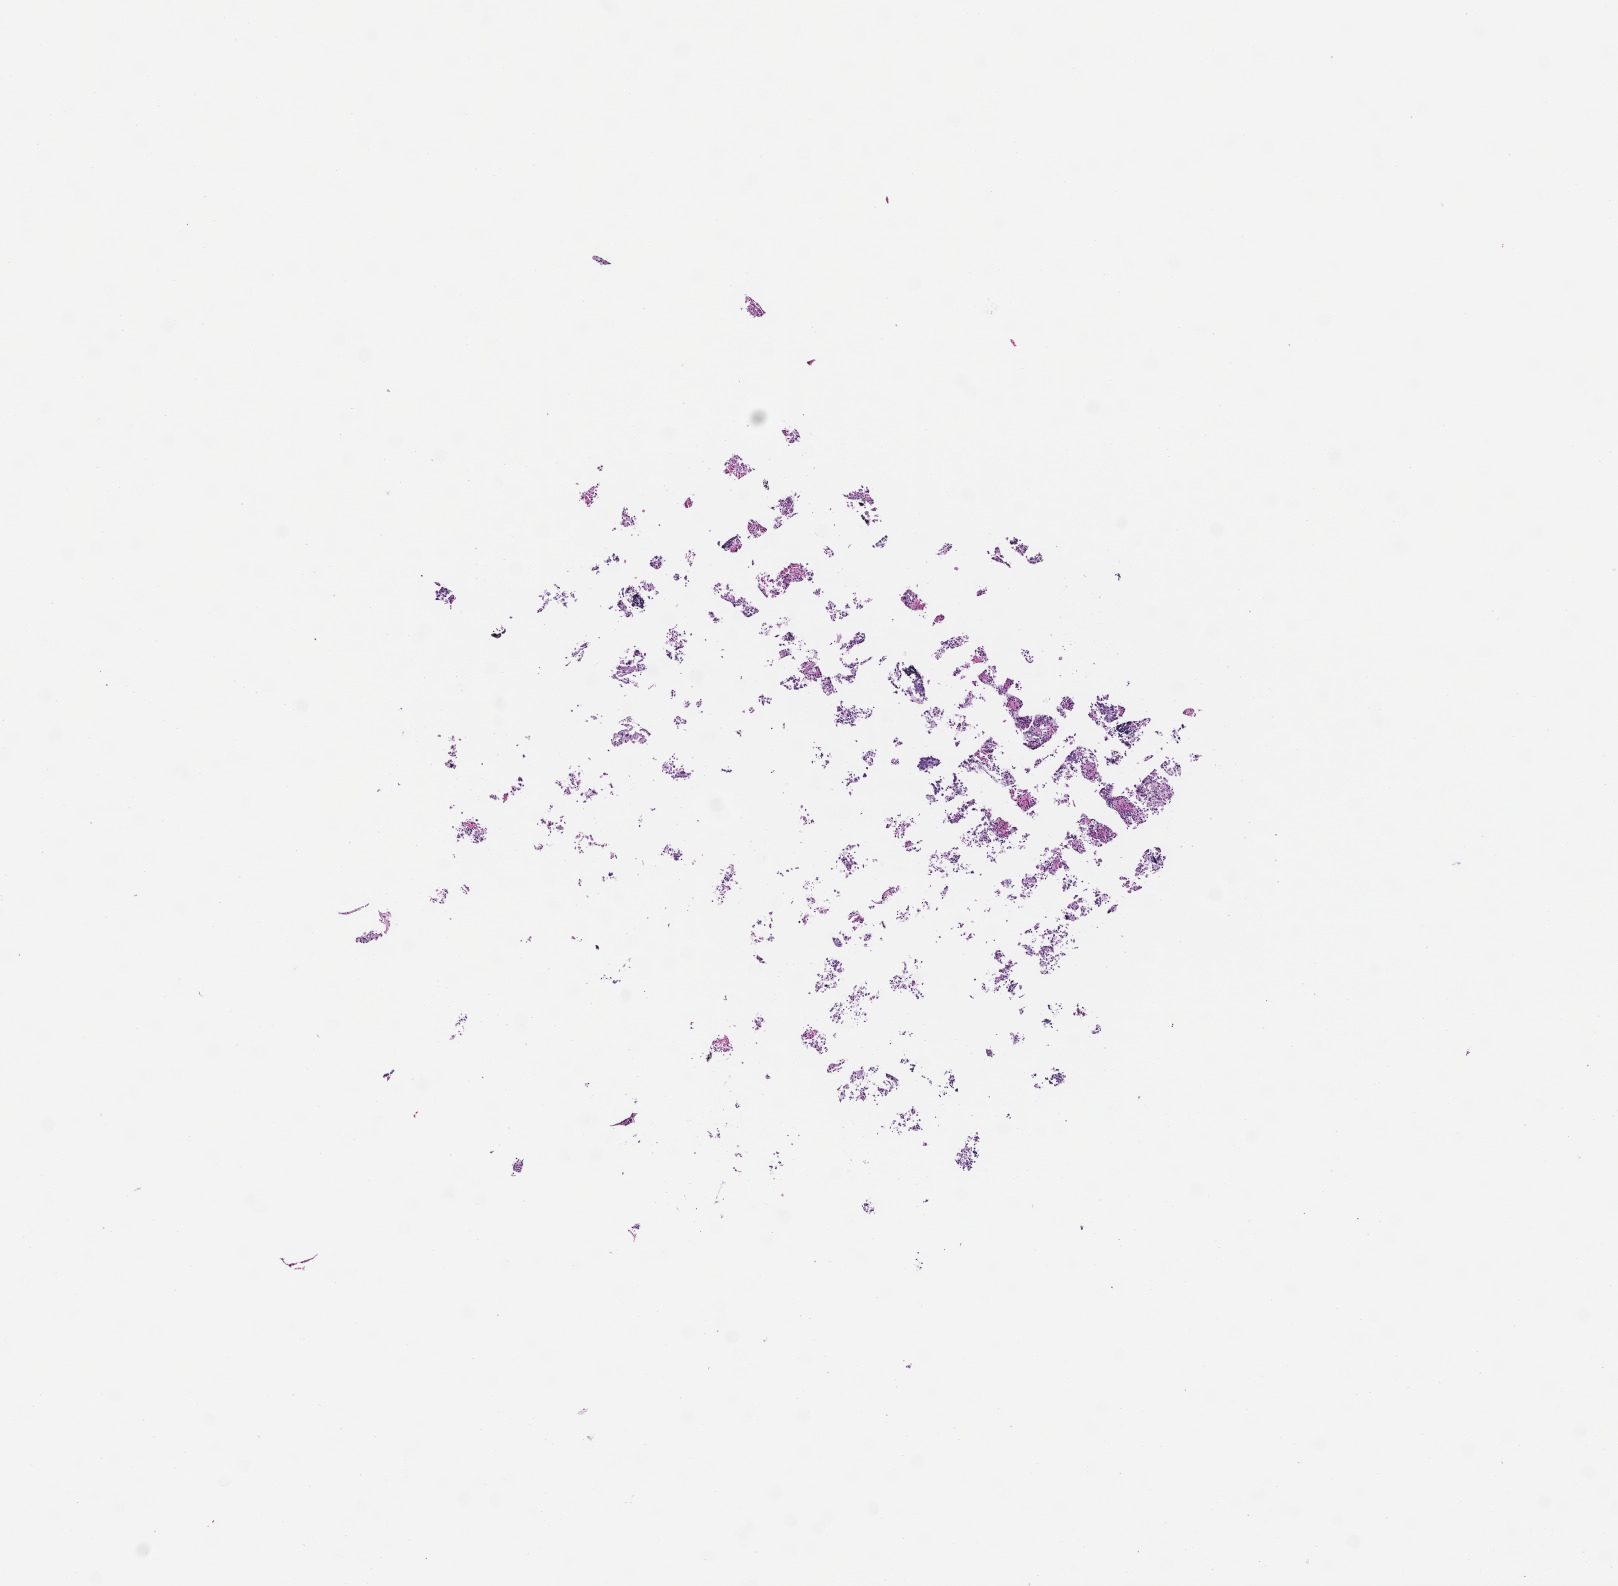
Digitized haematoxylin and eosin-stained section — a low-resolution overview of the entire scanned area, about 6.5 x 6.4 mm, FFPE section, tissue site: lung, archival tissue. Patient sex: female.
* this section: primary tumor
* diagnosis: Non-Small Cell Lung Carcinoma